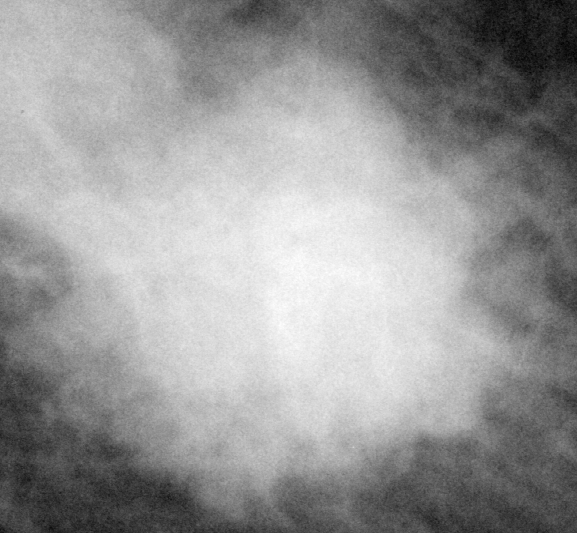
Crop from a digitized film mammogram around one marked abnormality, left breast, MLO view, BI-RADS breast density category 1 (scale 1–4).
- Finding: mass, shape lobulated, margins microlobulated; BI-RADS assessment category 5; subtlety rating 5 on a 1 (subtle) to 5 (obvious) scale; pathology result (as recorded, not read from the image): malignant.